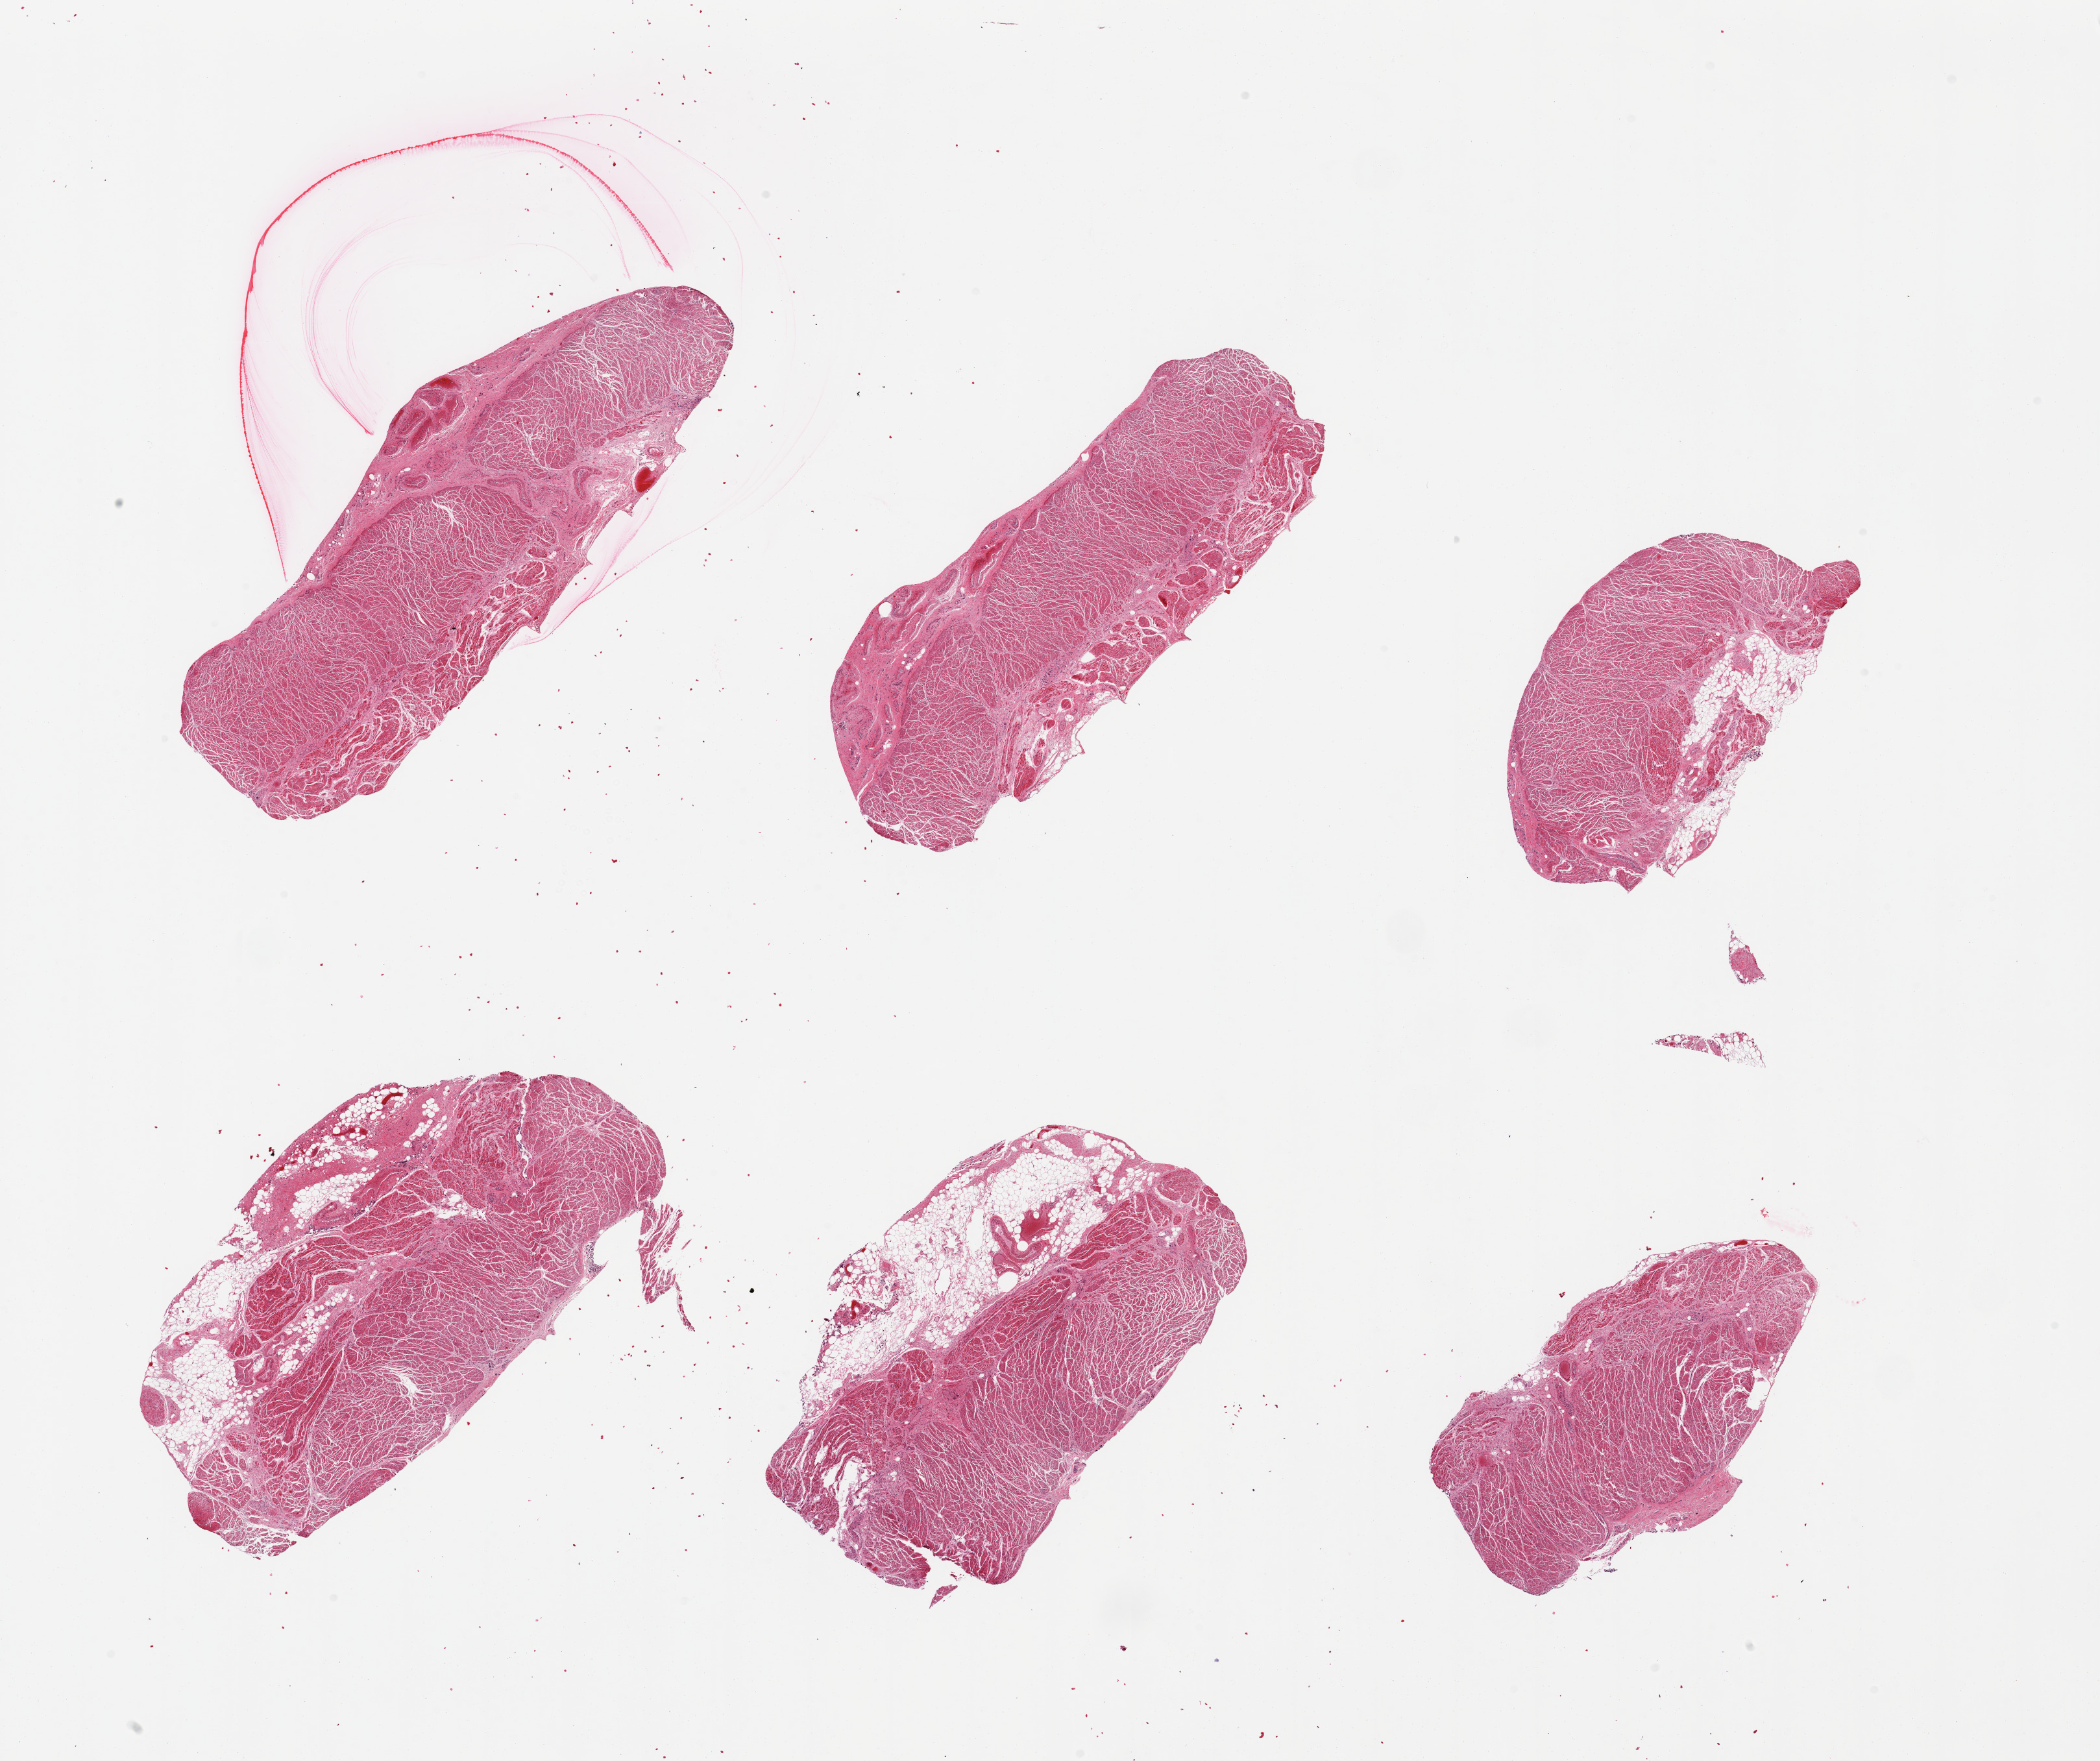
Digitized haematoxylin and eosin-stained section, brightfield — whole scanned area (about 25.6 x 21.5 mm, from a 20x scan) shown as a low-resolution overview, PAXgene-fixed, paraffin-embedded tissue, target tissue: gastroesophageal junction, tissue donor sample. Donor: male.
Pathologist's review note for this sample: 6 pieces; 30% external fat in 2 pieces.